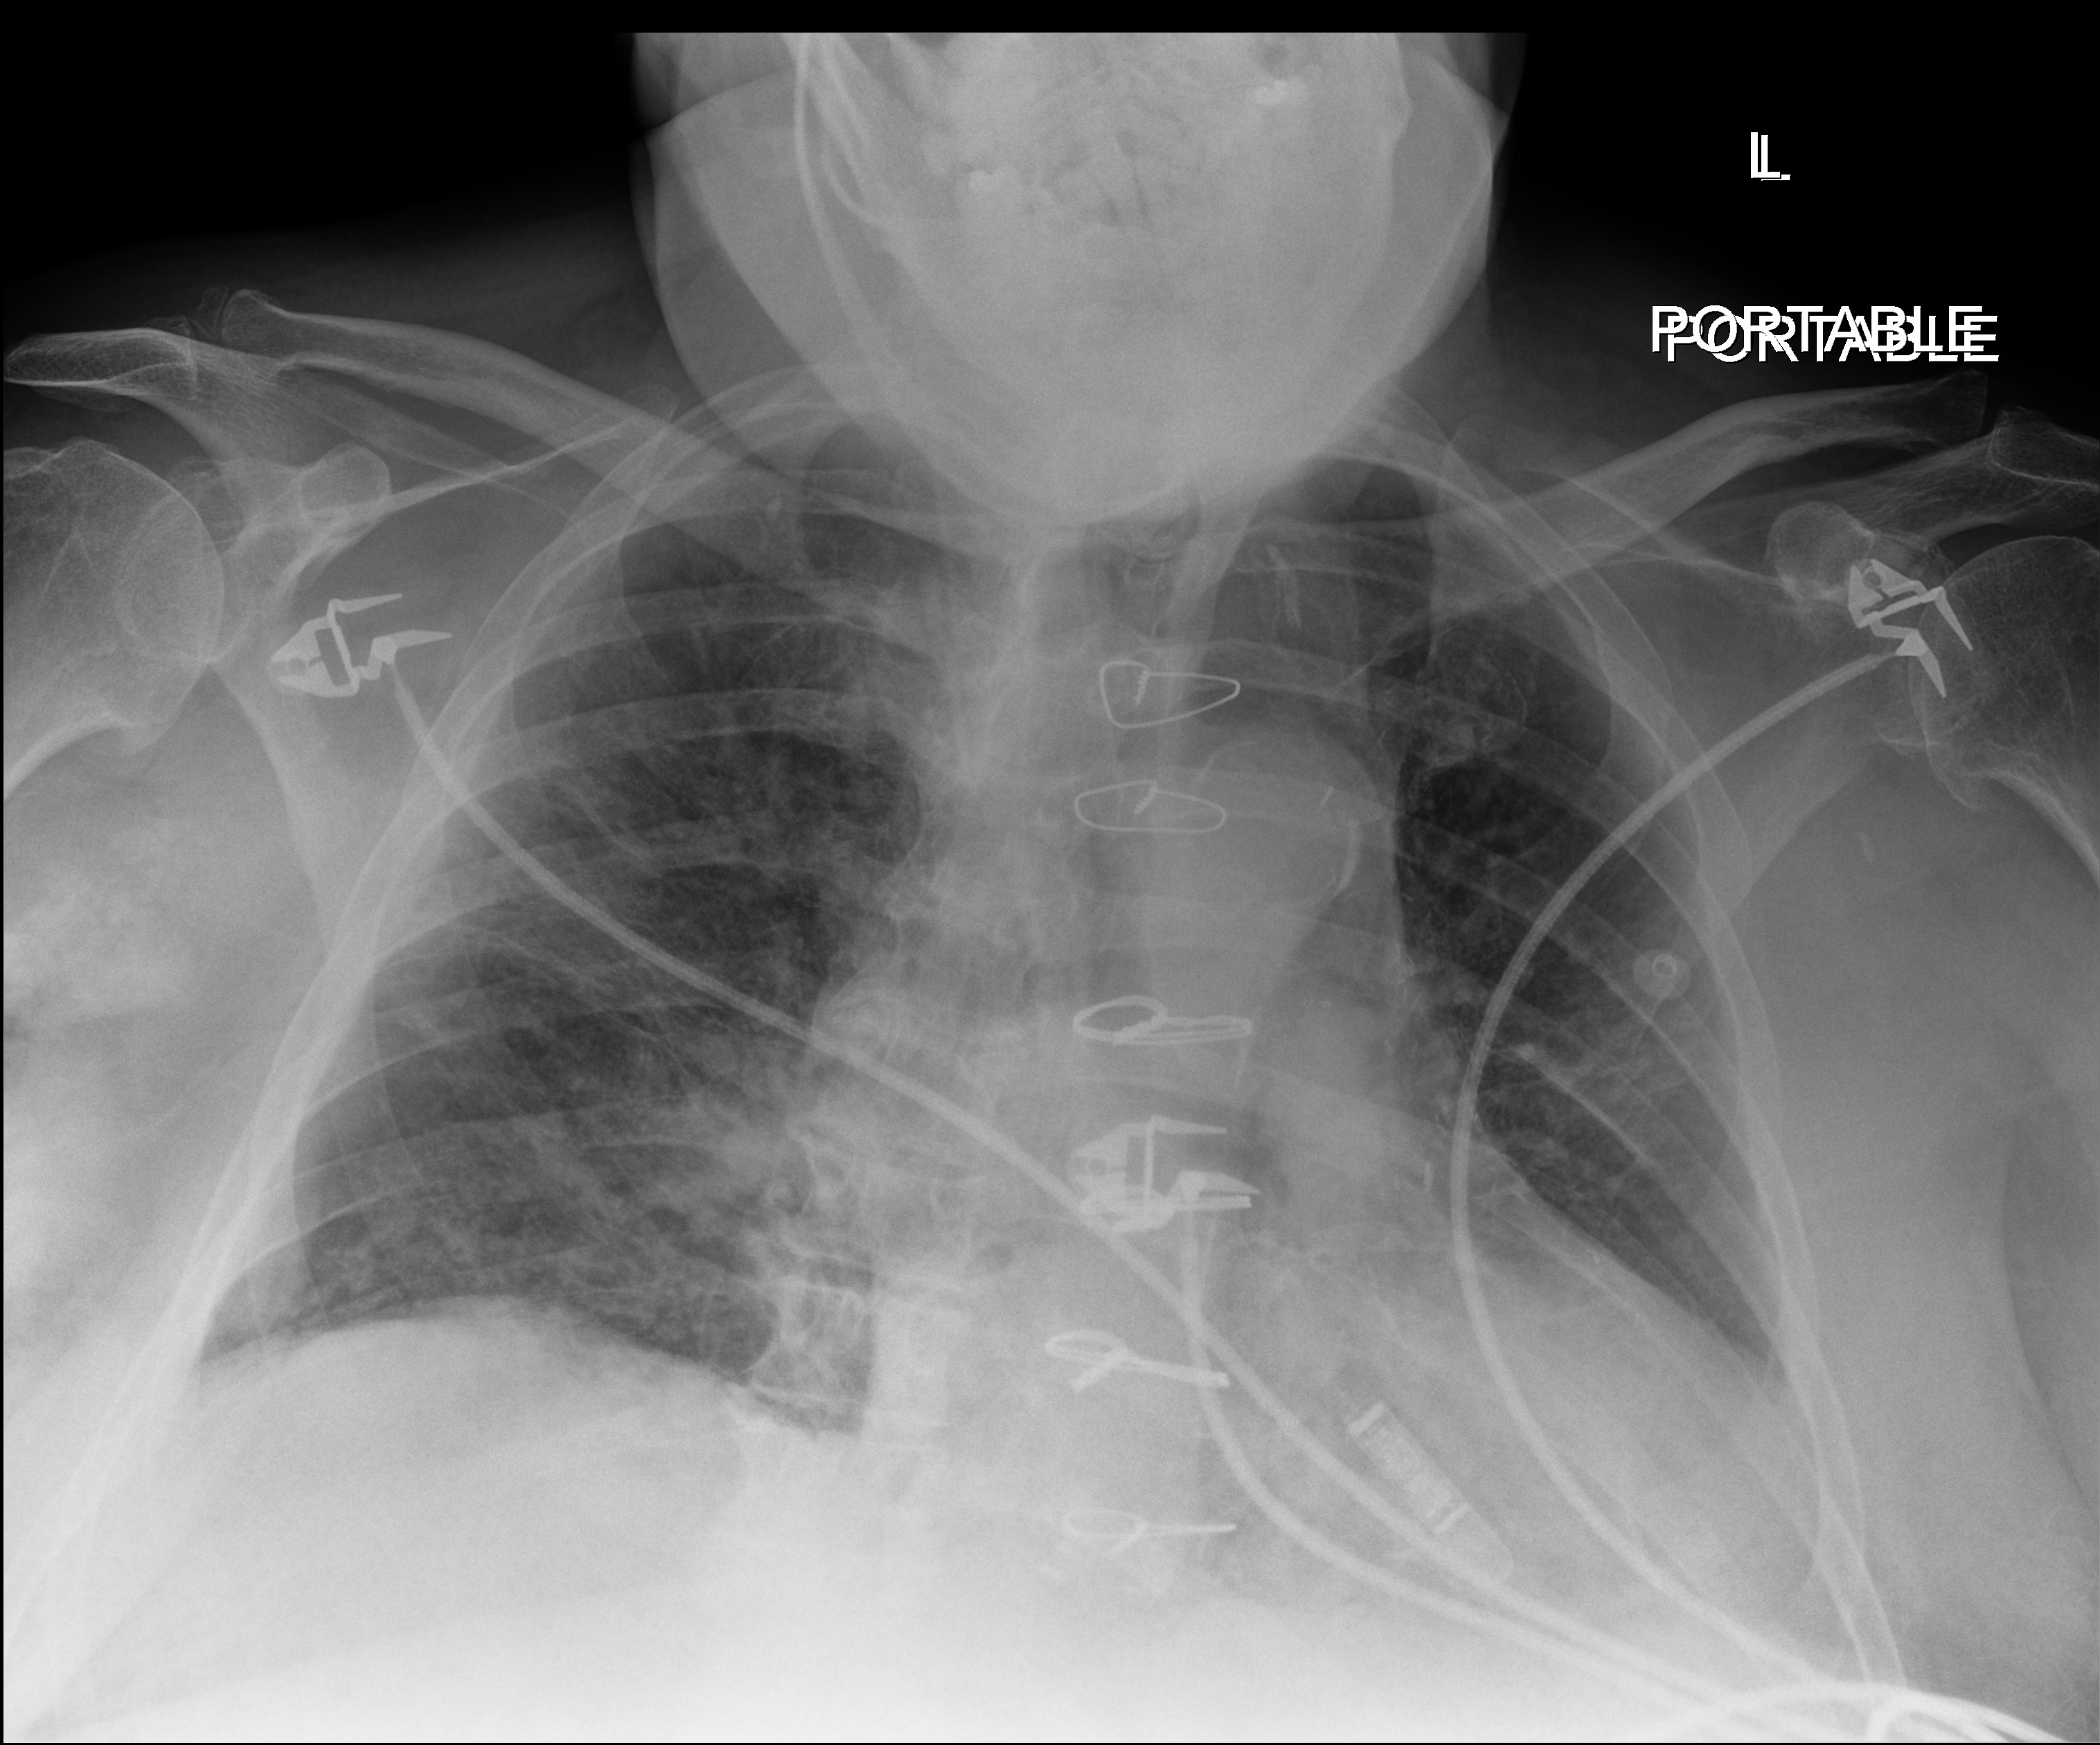
Chest X-ray (portable). Patient hospitalised with COVID-19; male, aged 60–74 years.
Admission-level facts for this patient (not findings on this image; timing relative to this image not recorded): length of hospital stay: 18 days; admitted to intensive care during this hospital stay: no.